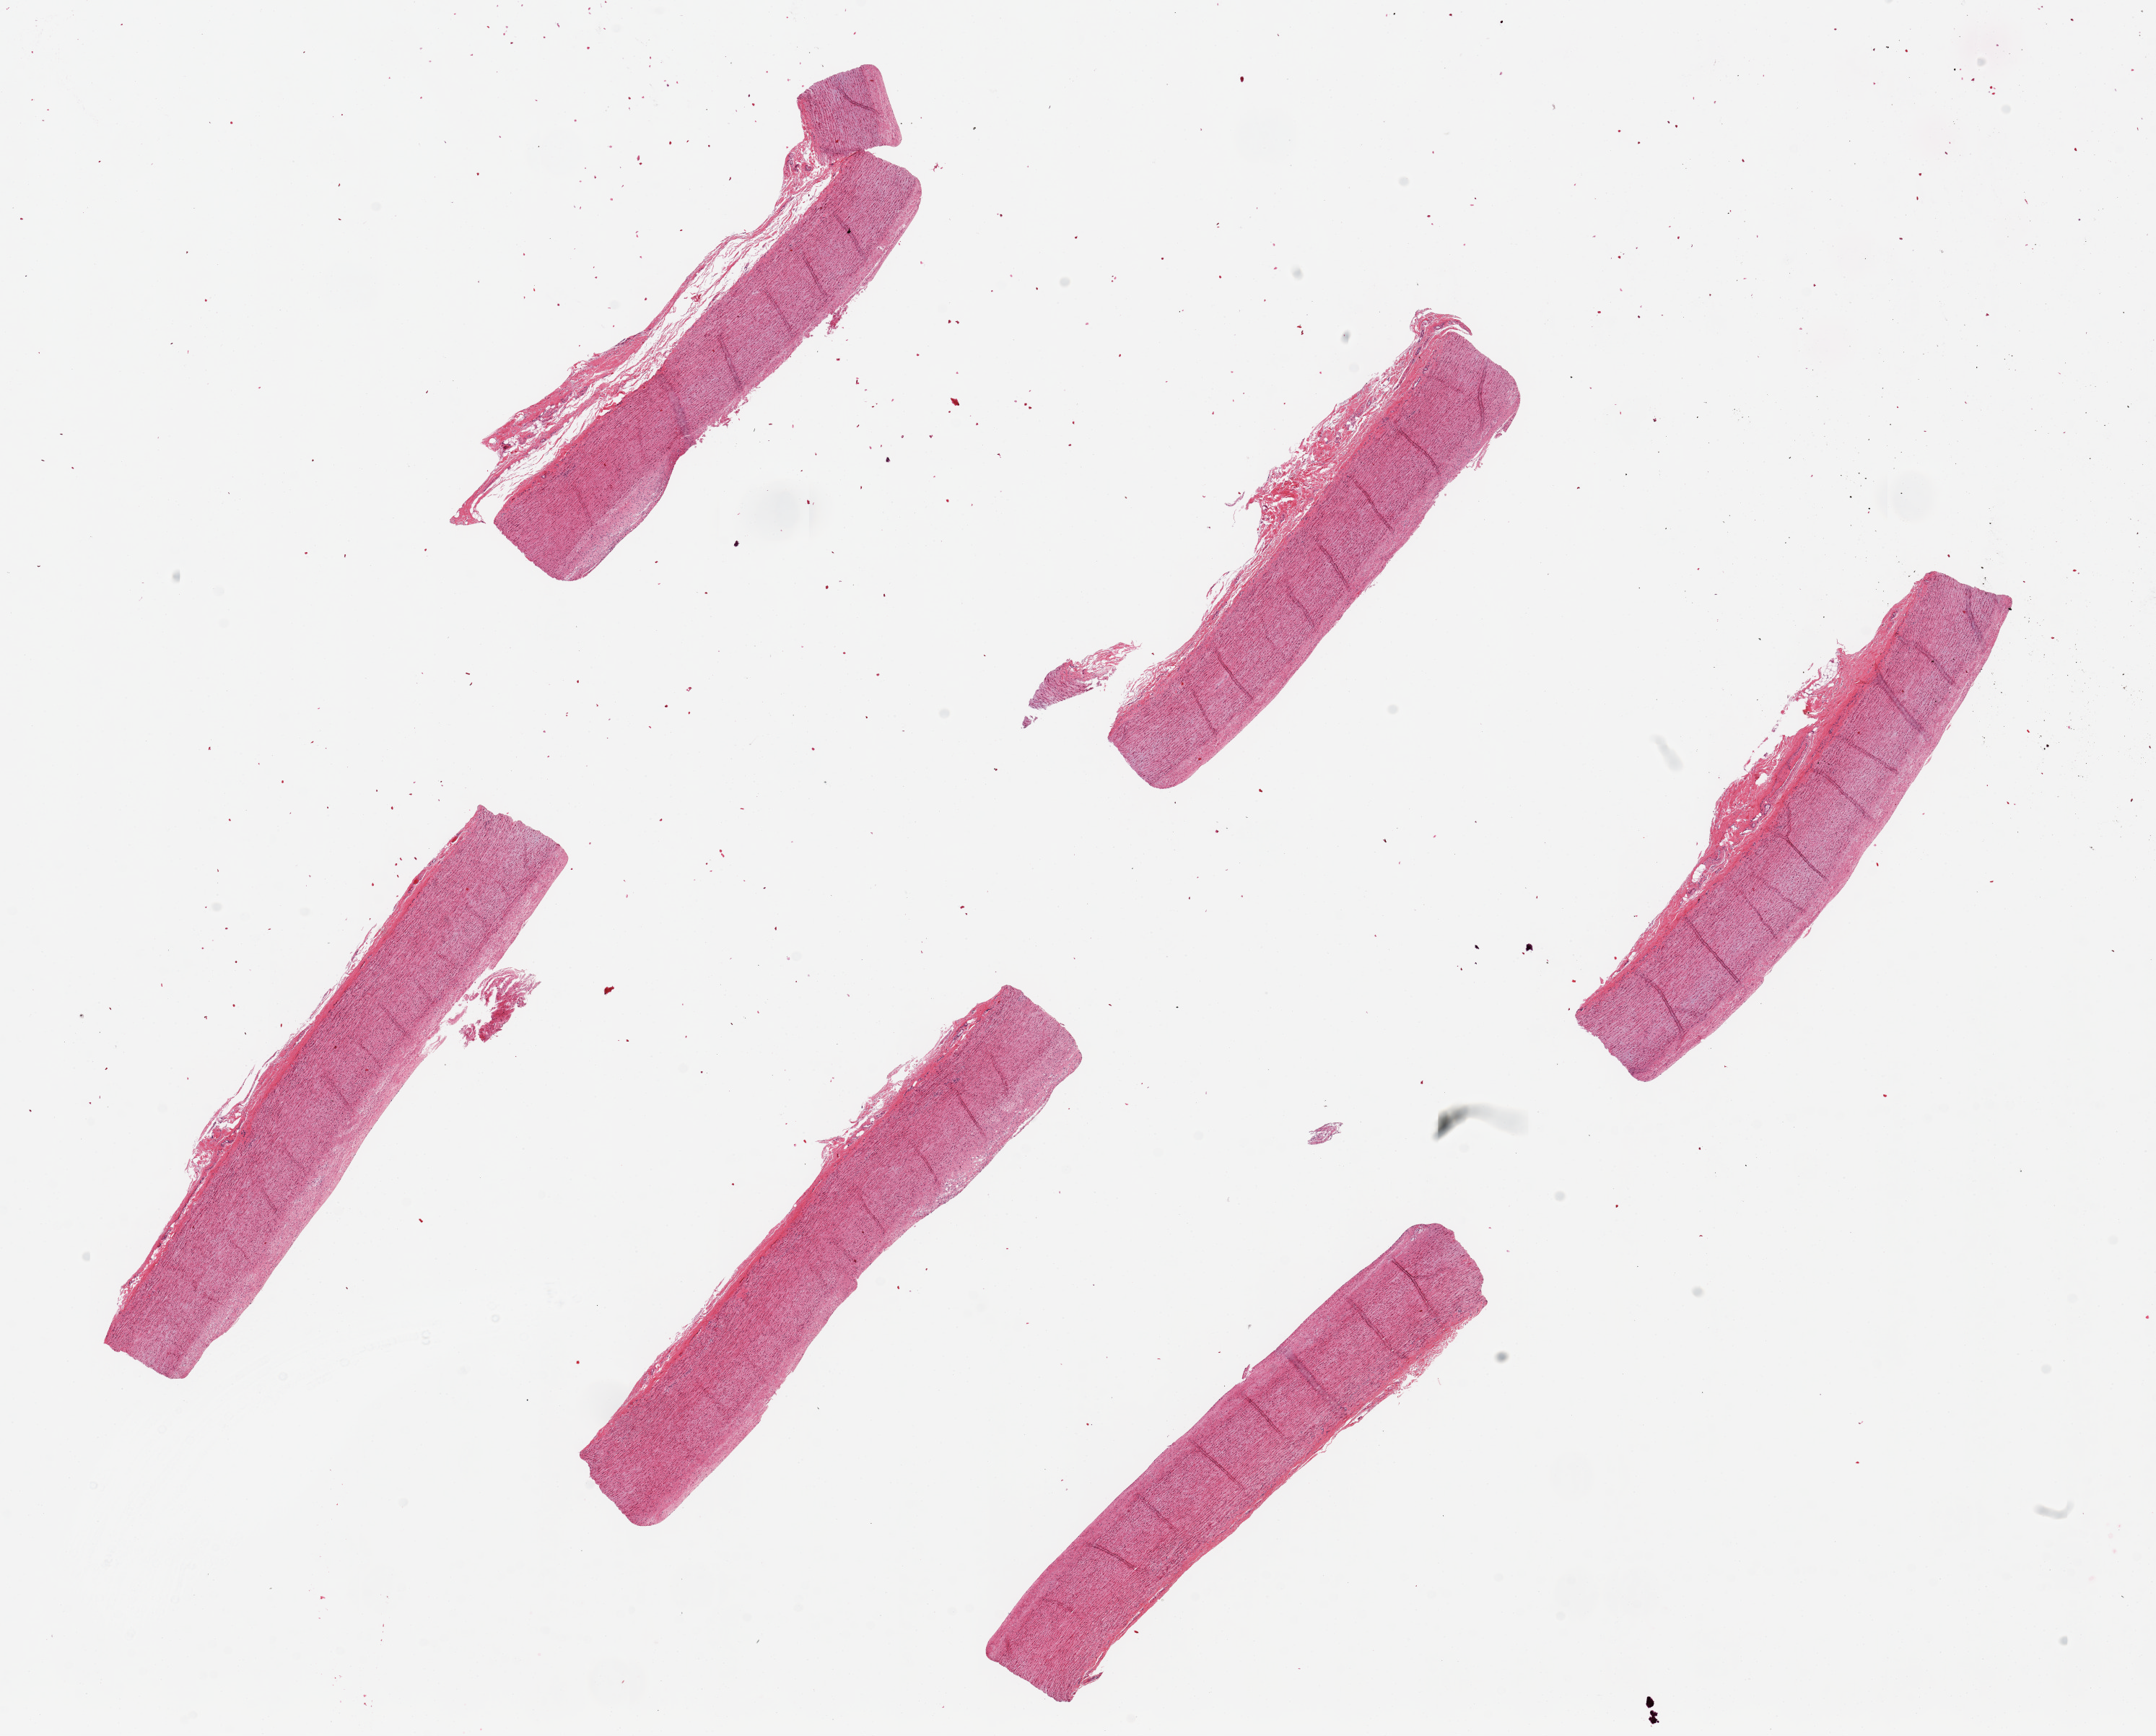
Digitized H&E-stained section, whole scanned area (about 23.6 x 19.0 mm) shown as a low-resolution overview; PAXgene-fixed paraffin-embedded (PFPE) section; sampled site (target tissue): aorta; donor tissue sample. Donor sex: female.
Reviewer comment on this tissue sample: 6 pieces ~7x1mm.